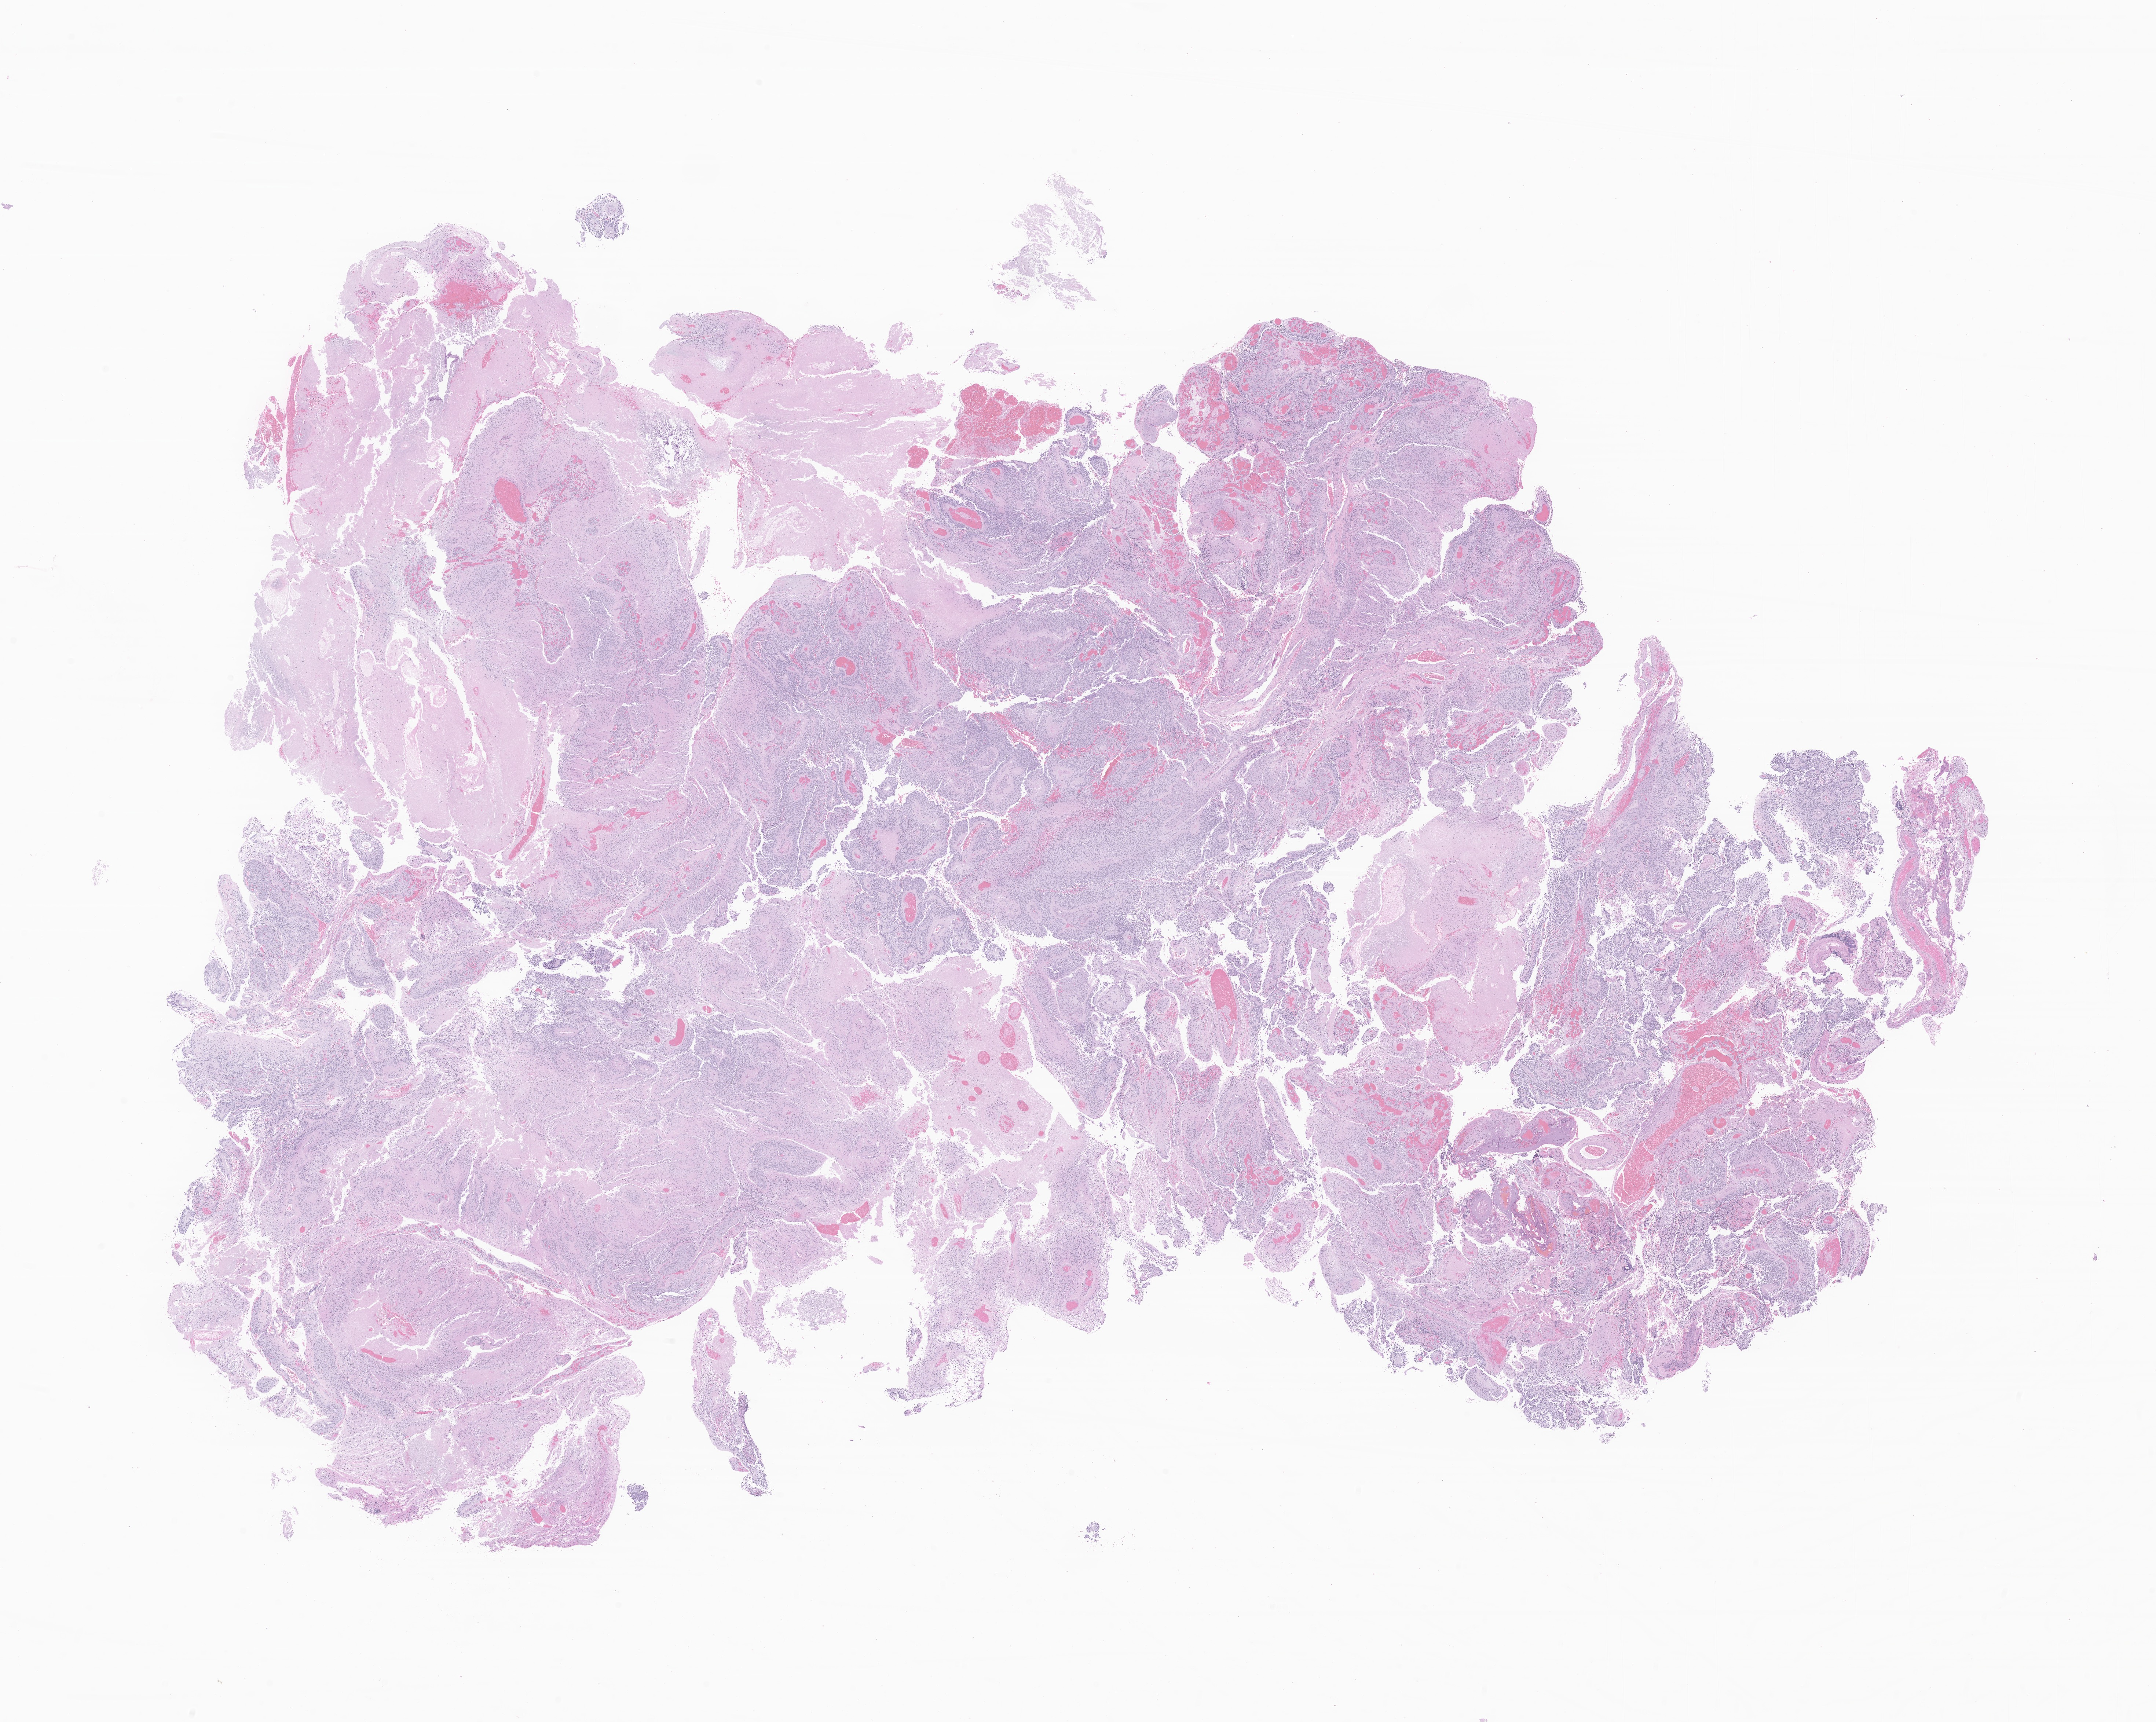
H&E whole-slide image of tumor tissue from the brain, shown as a low-resolution overview of the whole scanned area (about 24.8 x 19.8 mm), formalin-fixed, paraffin-embedded (FFPE) tissue. Male patient, age 849 days (about 2.3 years).
• recorded diagnosis: Ependymoma, NOS